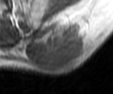
MRI of an extremity soft-tissue mass, one axial slice; slice 26 of 42 in the series (ordered by position); MR volume resampled by the dataset authors to the PET/CT grid (not the native acquisition matrix); 3.27 mm slice thickness; 113 × 94 image matrix. Male patient. From the clinical record (not read from this slice): histological type: leiomyosarcoma; grade: intermediate; site of the primary tumour: left pelvis.
Structures marked on this image (expert contour drawn on MRI and transferred to this co-registered scan by the dataset authors):
- gross tumour volume (mass): bounding box (x1, y1, x2, y2) in pixels: (24, 20, 89, 72)